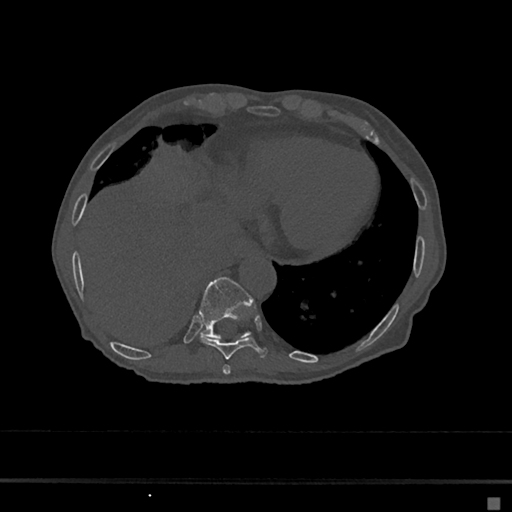
CT including the spine, one axial slice. Slice 256 of 797 in the series (ordered by position). Bone window (W 1800 / L 400 HU). 0.5 mm slice thickness. 512 × 512 image matrix, field of view 360 × 360 mm. Patient: female, 68 years. From the clinical record (not read from this slice): primary cancer: renal.
Structures marked on this image (semi-automatically segmented with operator editing):
- T10 vertebra: box from (x=199, y=277) to (x=253, y=339) px
- T8 vertebra: (x=222, y=364)–(x=231, y=375)
- T9 vertebra: (x=200, y=319)–(x=268, y=359)